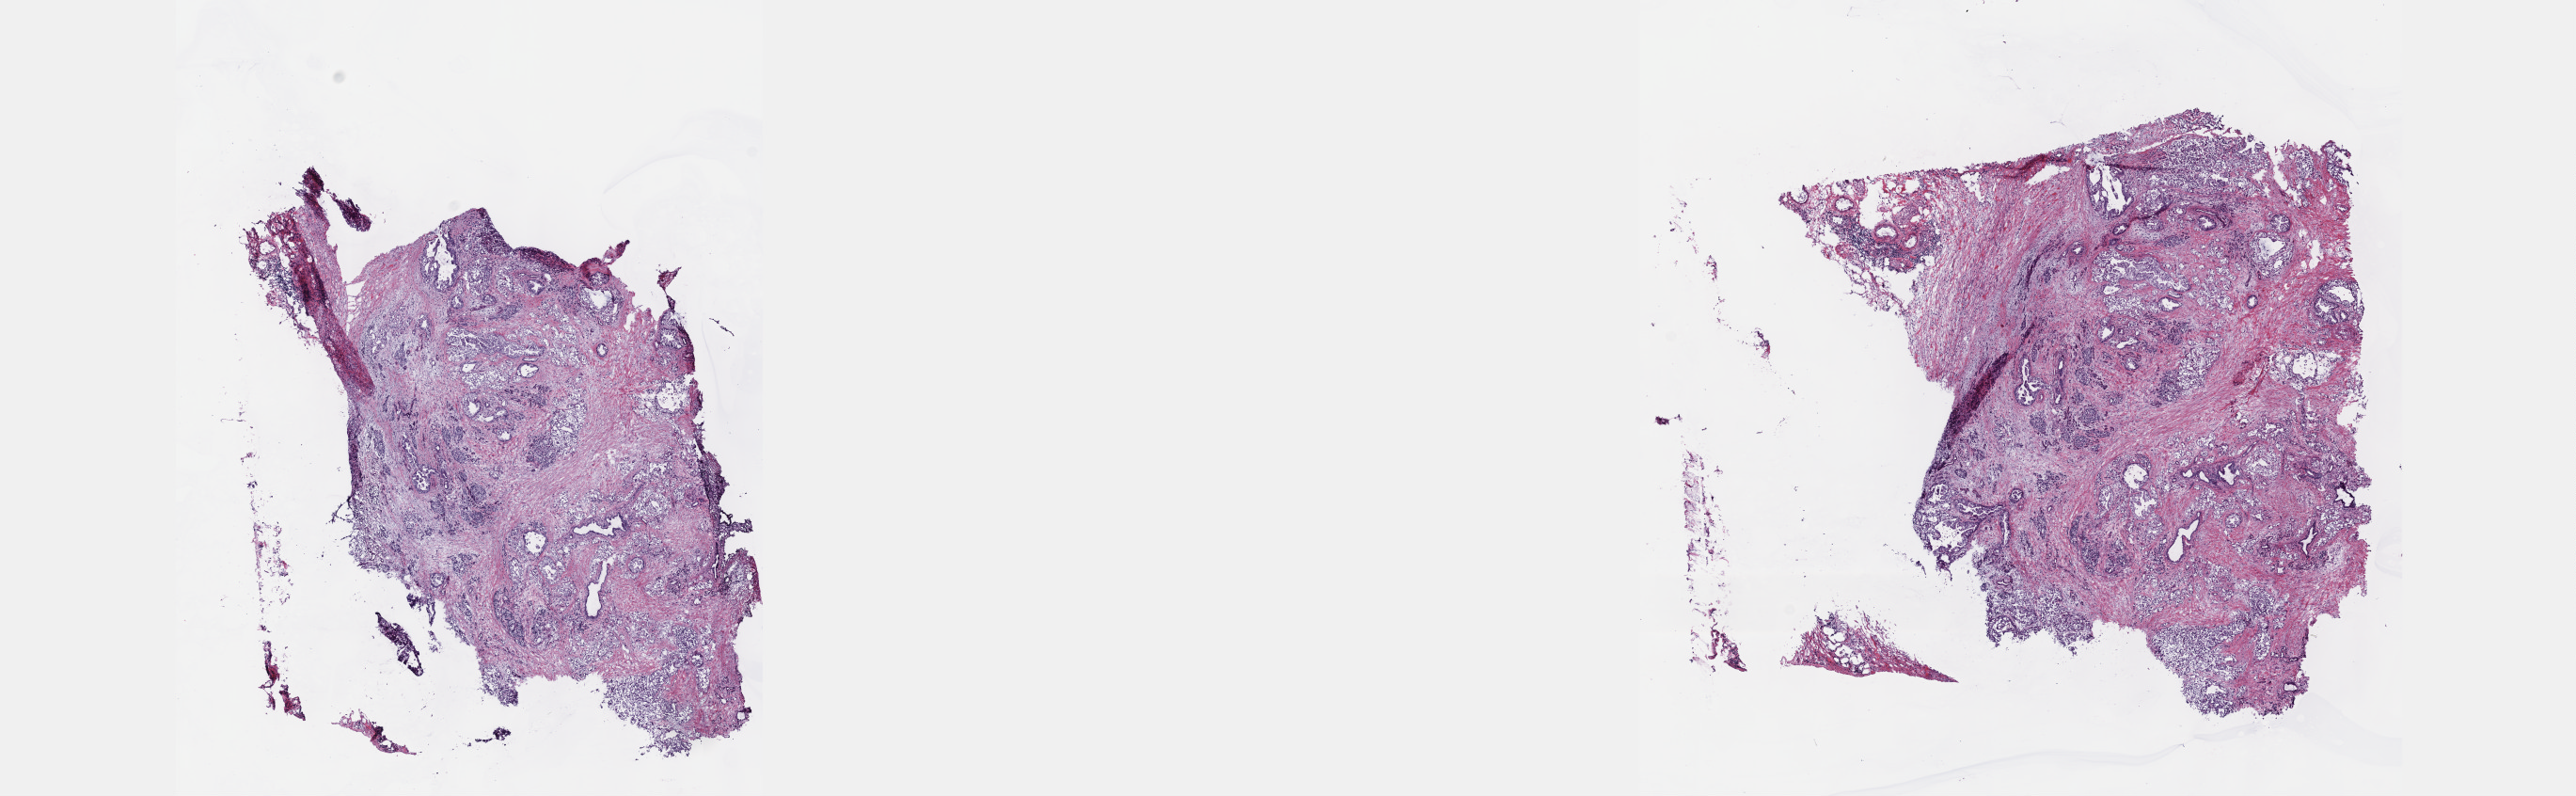
Whole-slide histology image, H&E-stained, a low-resolution overview of the entire scanned area, about 22.1 x 6.8 mm. Frozen section from the top of the tissue portion. Sample: primary tumour, pancreas. Patient: male, age at initial diagnosis 61 years. Histologic grade: G3 (poorly differentiated). Pathologist review of this section (percent, as recorded): tumour cells 35%, tumour nuclei 35%, normal cells 20%, stromal cells 45%, necrosis 0%. Inflammatory infiltration, as recorded: lymphocyte infiltration 4%, monocyte infiltration 2%, neutrophil infiltration 7%.
* pathologic diagnosis: Adenocarcinoma, NOS (body of pancreas)
* AJCC pathologic stage: IIA (7th edition)